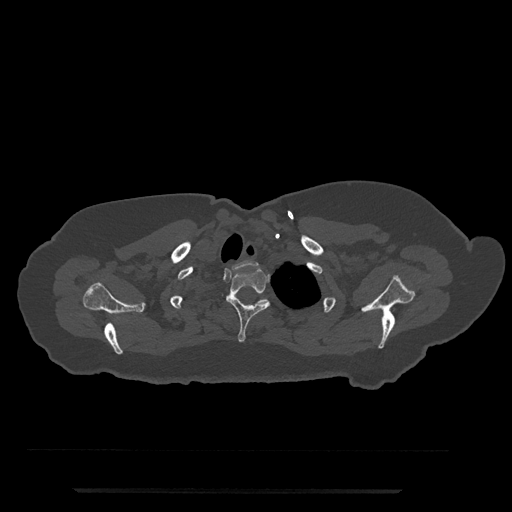
CT including the spine, one axial slice. Position 670 of 797 along the scan axis. 120 kVp. Bone window (W 1800 / L 400 HU). 0.5 mm slice thickness. 512 × 512 image matrix, field of view 440 × 440 mm. Patient: female, 51 years. From the clinical record (not read from this slice): primary cancer: neuro; vertebrae with lytic lesions (as recorded): T8.
Annotated regions visible in this slice (semi-automatically segmented with operator editing):
- T1 vertebra: box from (x=232, y=260) to (x=257, y=269) px
- T2 vertebra: (x=226, y=268)–(x=270, y=342)
- T3 vertebra: (x=234, y=293)–(x=269, y=303)